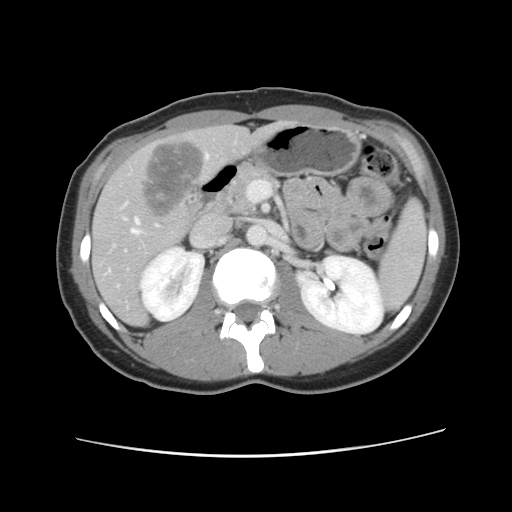
Contrast-enhanced abdominal CT, one axial slice; position 49 of 134 along the scan axis; 120 kVp; intravenous contrast given; soft-tissue window (W 400 / L 40 HU); 512 × 512 image matrix. Female patient, age 33 years. From the clinical record (not read from this slice): diagnosis: colorectal cancer liver metastases, imaged before liver resection; multiple liver metastases: yes; largest metastasis: 4.5 cm; disease in both lobes: yes.
Structures marked on this image (manually delineated by an expert):
- hepatic veins: bounding box (x1, y1, x2, y2) in pixels: (132, 155, 209, 234)
- liver: (92, 124, 286, 325)
- planned liver remnant (the part of the liver to remain after resection): (92, 124, 285, 325)
- liver metastasis: (140, 140, 206, 221)